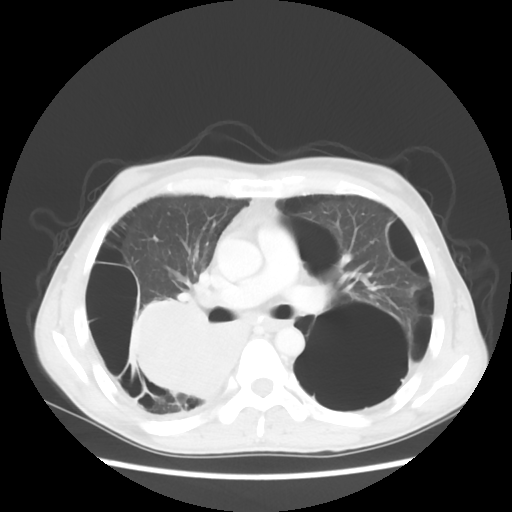
Chest CT, one axial slice. Position 32 of 56 along the scan axis. Reconstruction kernel STANDARD. 140 kVp. Lung window (W 1500 / L -600 HU). 5 mm slice thickness. 512 × 512 image matrix, field of view 351 × 351 mm. Patient: male, 41 years. From the clinical record (not read from this slice): clinical TNM (as recorded): T4 N0 M1a; histopathological grade: G3.
Structures marked on this image (rectangle marked by the reading radiologist):
- lung tumour (recorded histology: large cell carcinoma): box from (x=131, y=288) to (x=237, y=412) px